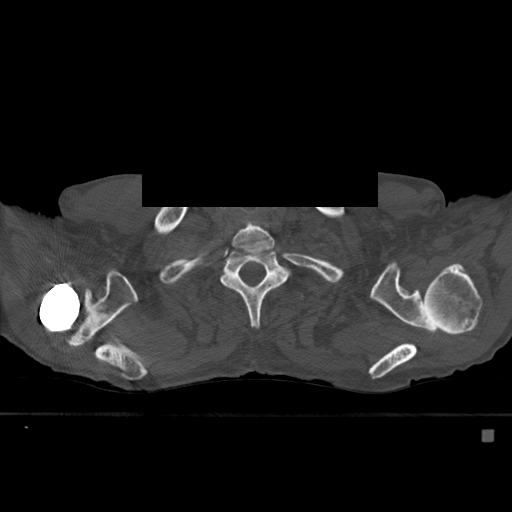
CT including the spine, one axial slice. Position 447 of 527 along the scan axis. Bone window (W 1800 / L 400 HU). 512 × 512 image matrix, field of view 373 × 373 mm. Male patient, age 78 years. From the clinical record (not read from this slice): primary cancer: prostate.
Outlined on this slice (semi-automatic segmentation, software-assisted and operator-edited):
- T1 vertebra: bounding box (x1, y1, x2, y2) in pixels: (233, 227, 275, 248)
- T2 vertebra: (220, 241, 289, 327)
- T3 vertebra: (299, 293, 303, 299)